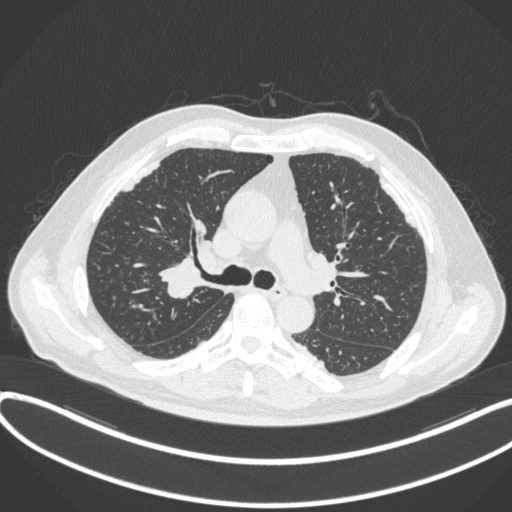
Chest CT, one axial slice. Slice 272 of 455 in the series (ordered by position). Reconstruction kernel B31f. Lung window (W 1500 / L -600 HU). 1 mm slice thickness. 512 × 512 image matrix, field of view 400 × 400 mm. Male patient, age 58 years. Case-level facts recorded for this patient, not image findings: clinical TNM (as recorded): T1c N0 M0.
Structures marked on this image (bounding box drawn by a radiologist):
- lung tumour (recorded histology: squamous cell carcinoma): bounding box <158,256,204,302> (left, top, right, bottom; pixels)